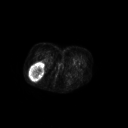
FDG PET of an extremity soft-tissue mass (from a PET/CT study), one axial slice. Slice 43 of 267 in the series (ordered by position). 128 × 128 image matrix, field of view 700 × 700 mm. Female patient, age 70 years. From the clinical record (not read from this slice): histological type: synovial sarcoma; grade: intermediate; site of the primary tumour: right buttock.
Annotated regions visible in this slice (expert contour drawn on MRI and transferred to this co-registered scan by the dataset authors):
- gross tumour volume including surrounding oedema: bounding box [x1, y1, x2, y2] px = [29, 62, 45, 80]
- gross tumour volume (mass): [29, 62, 45, 80]